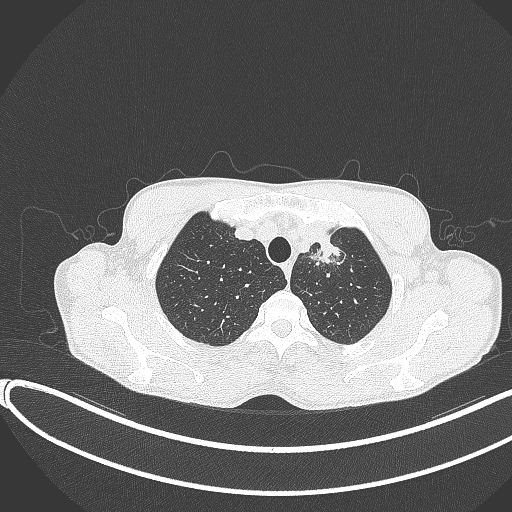
Chest CT, one axial slice. Slice 329 of 374 in the series (ordered by position). Reconstruction kernel B70f. 120 kVp. Lung window (W 1500 / L -600 HU). 512 × 512 image matrix, field of view 400 × 400 mm. Male patient, age 58 years. From the clinical record (not read from this slice): clinical TNM (as recorded): T1c N1 M0.
Outlined on this slice (rectangle marked by the reading radiologist):
- lung tumour (recorded histology: adenocarcinoma): bounding box (x1, y1, x2, y2) in pixels: (302, 222, 345, 265)